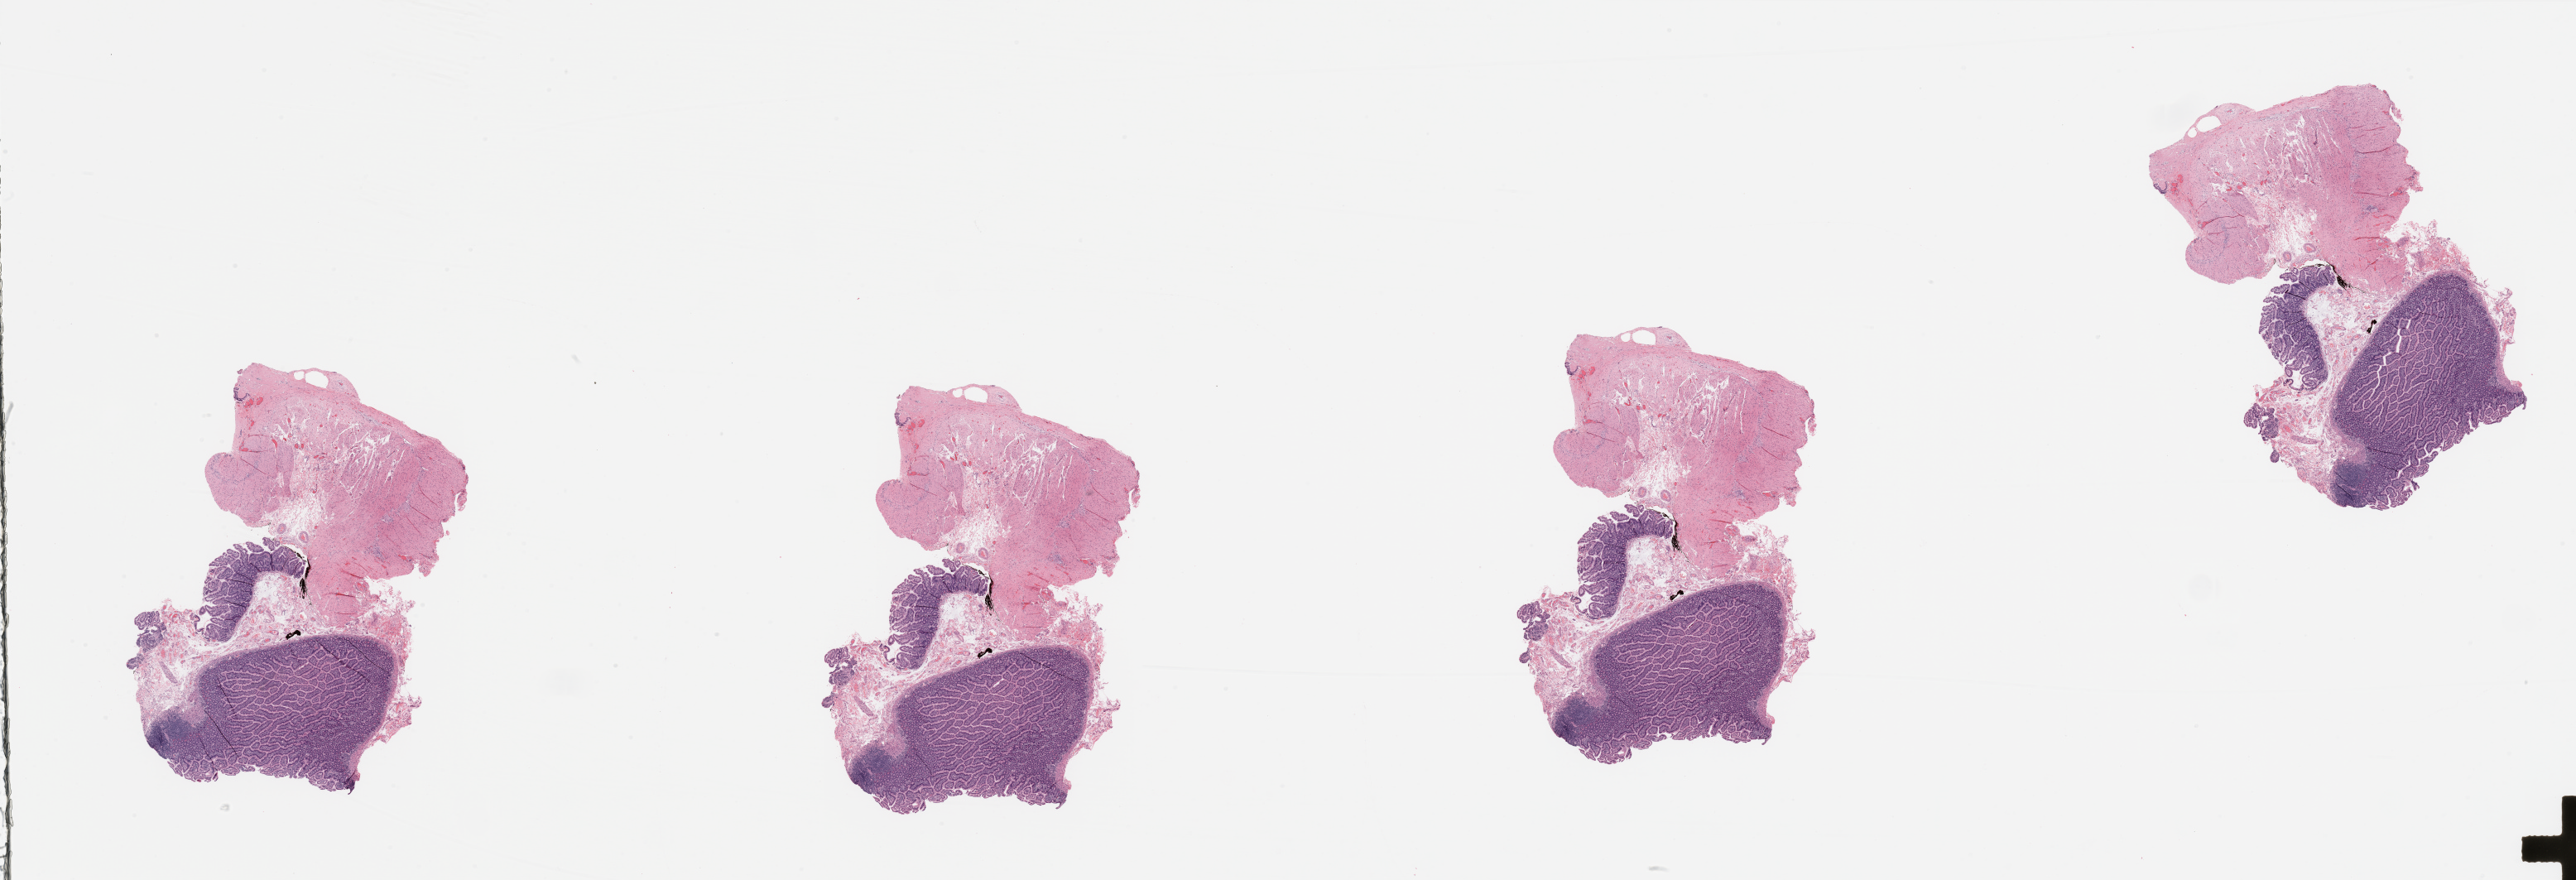
Digitized H&E-stained tissue section (whole slide) — a low-resolution overview of the entire scanned area, about 49.2 x 16.8 mm. Pancreas, normal (non-tumour) tissue. Female, 78 y/o.
• this section: normal (non-tumour) tissue from the same patient
• patient diagnosis: Infiltrating duct carcinoma, NOS